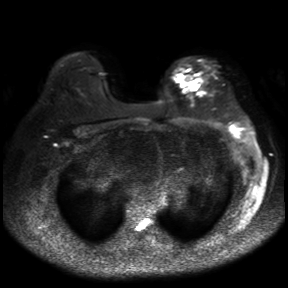
Breast MRI, one axial slice. Diffusion-weighted series; image 2 of 4 stored at this slice position (different b-values; order by instance number). 3 T. 4 mm slice thickness. 288 × 288 image matrix, field of view 360 × 360 mm. Female patient.
Outlined on this slice (expert manual segmentation):
- tumour on diffusion-weighted imaging: bounding box [x1, y1, x2, y2] px = [188, 79, 198, 90]